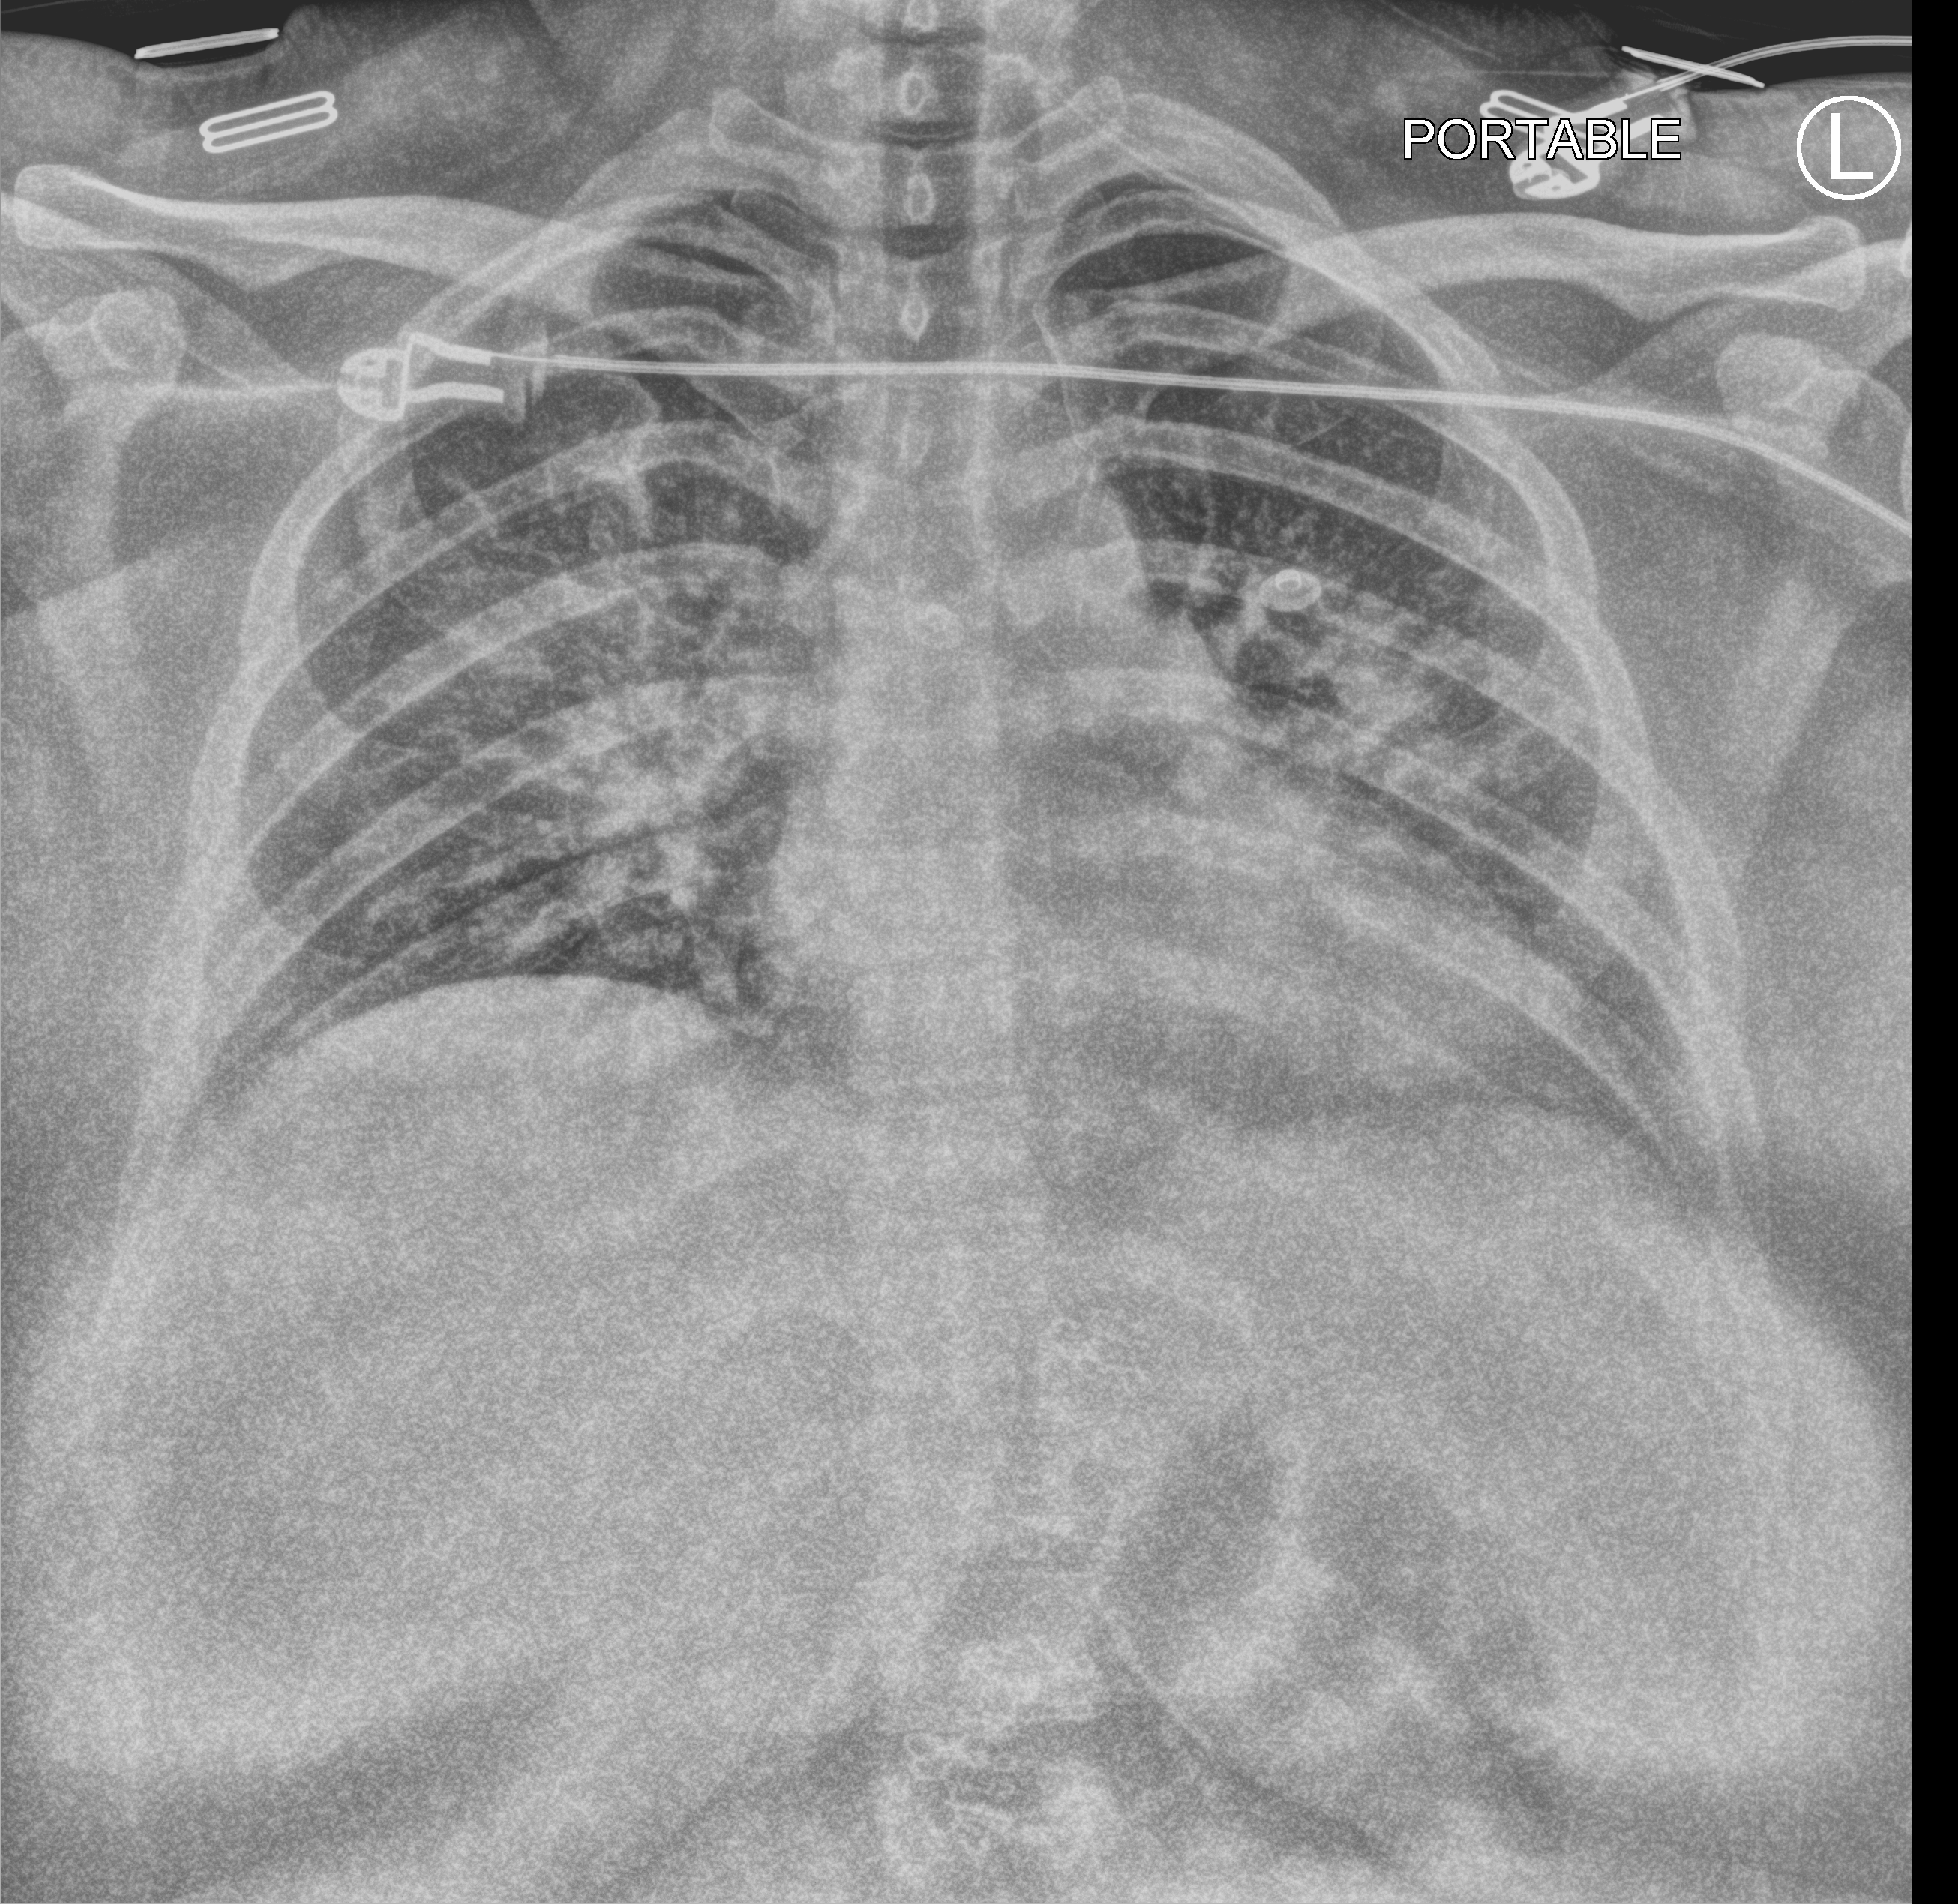
Portable chest radiograph; anteroposterior (AP) projection. Patient hospitalised with COVID-19; female, aged 18–59 years.
Hospital-stay facts (about this admission, not read from this image; timing relative to this image not recorded):
- other chronic lung disease (admission record): no
- admitted to intensive care during this hospital stay: no